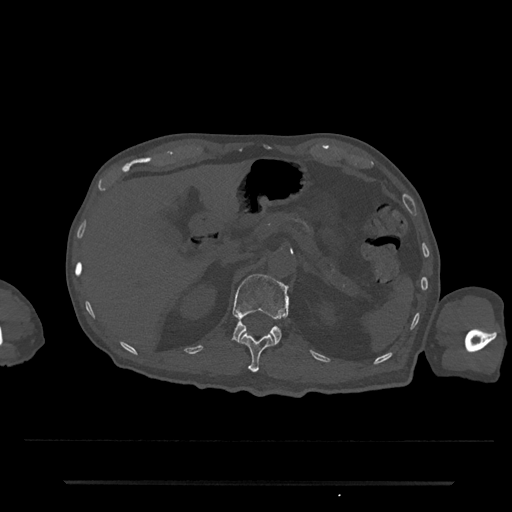
CT including the spine, one axial slice; position 164 of 797 along the scan axis; reconstruction kernel Br40s/3; 120 kVp; bone window (W 1800 / L 400 HU); 0.5 mm slice thickness; 512 × 512 image matrix. Male patient, age 74 years. From the clinical record (not read from this slice): primary cancer: prostate.
Structures marked on this image (semi-automatically segmented with operator editing):
- L1 vertebra: bounding box (x1, y1, x2, y2) in pixels: (233, 274, 290, 345)
- T12 vertebra: (240, 333, 273, 373)